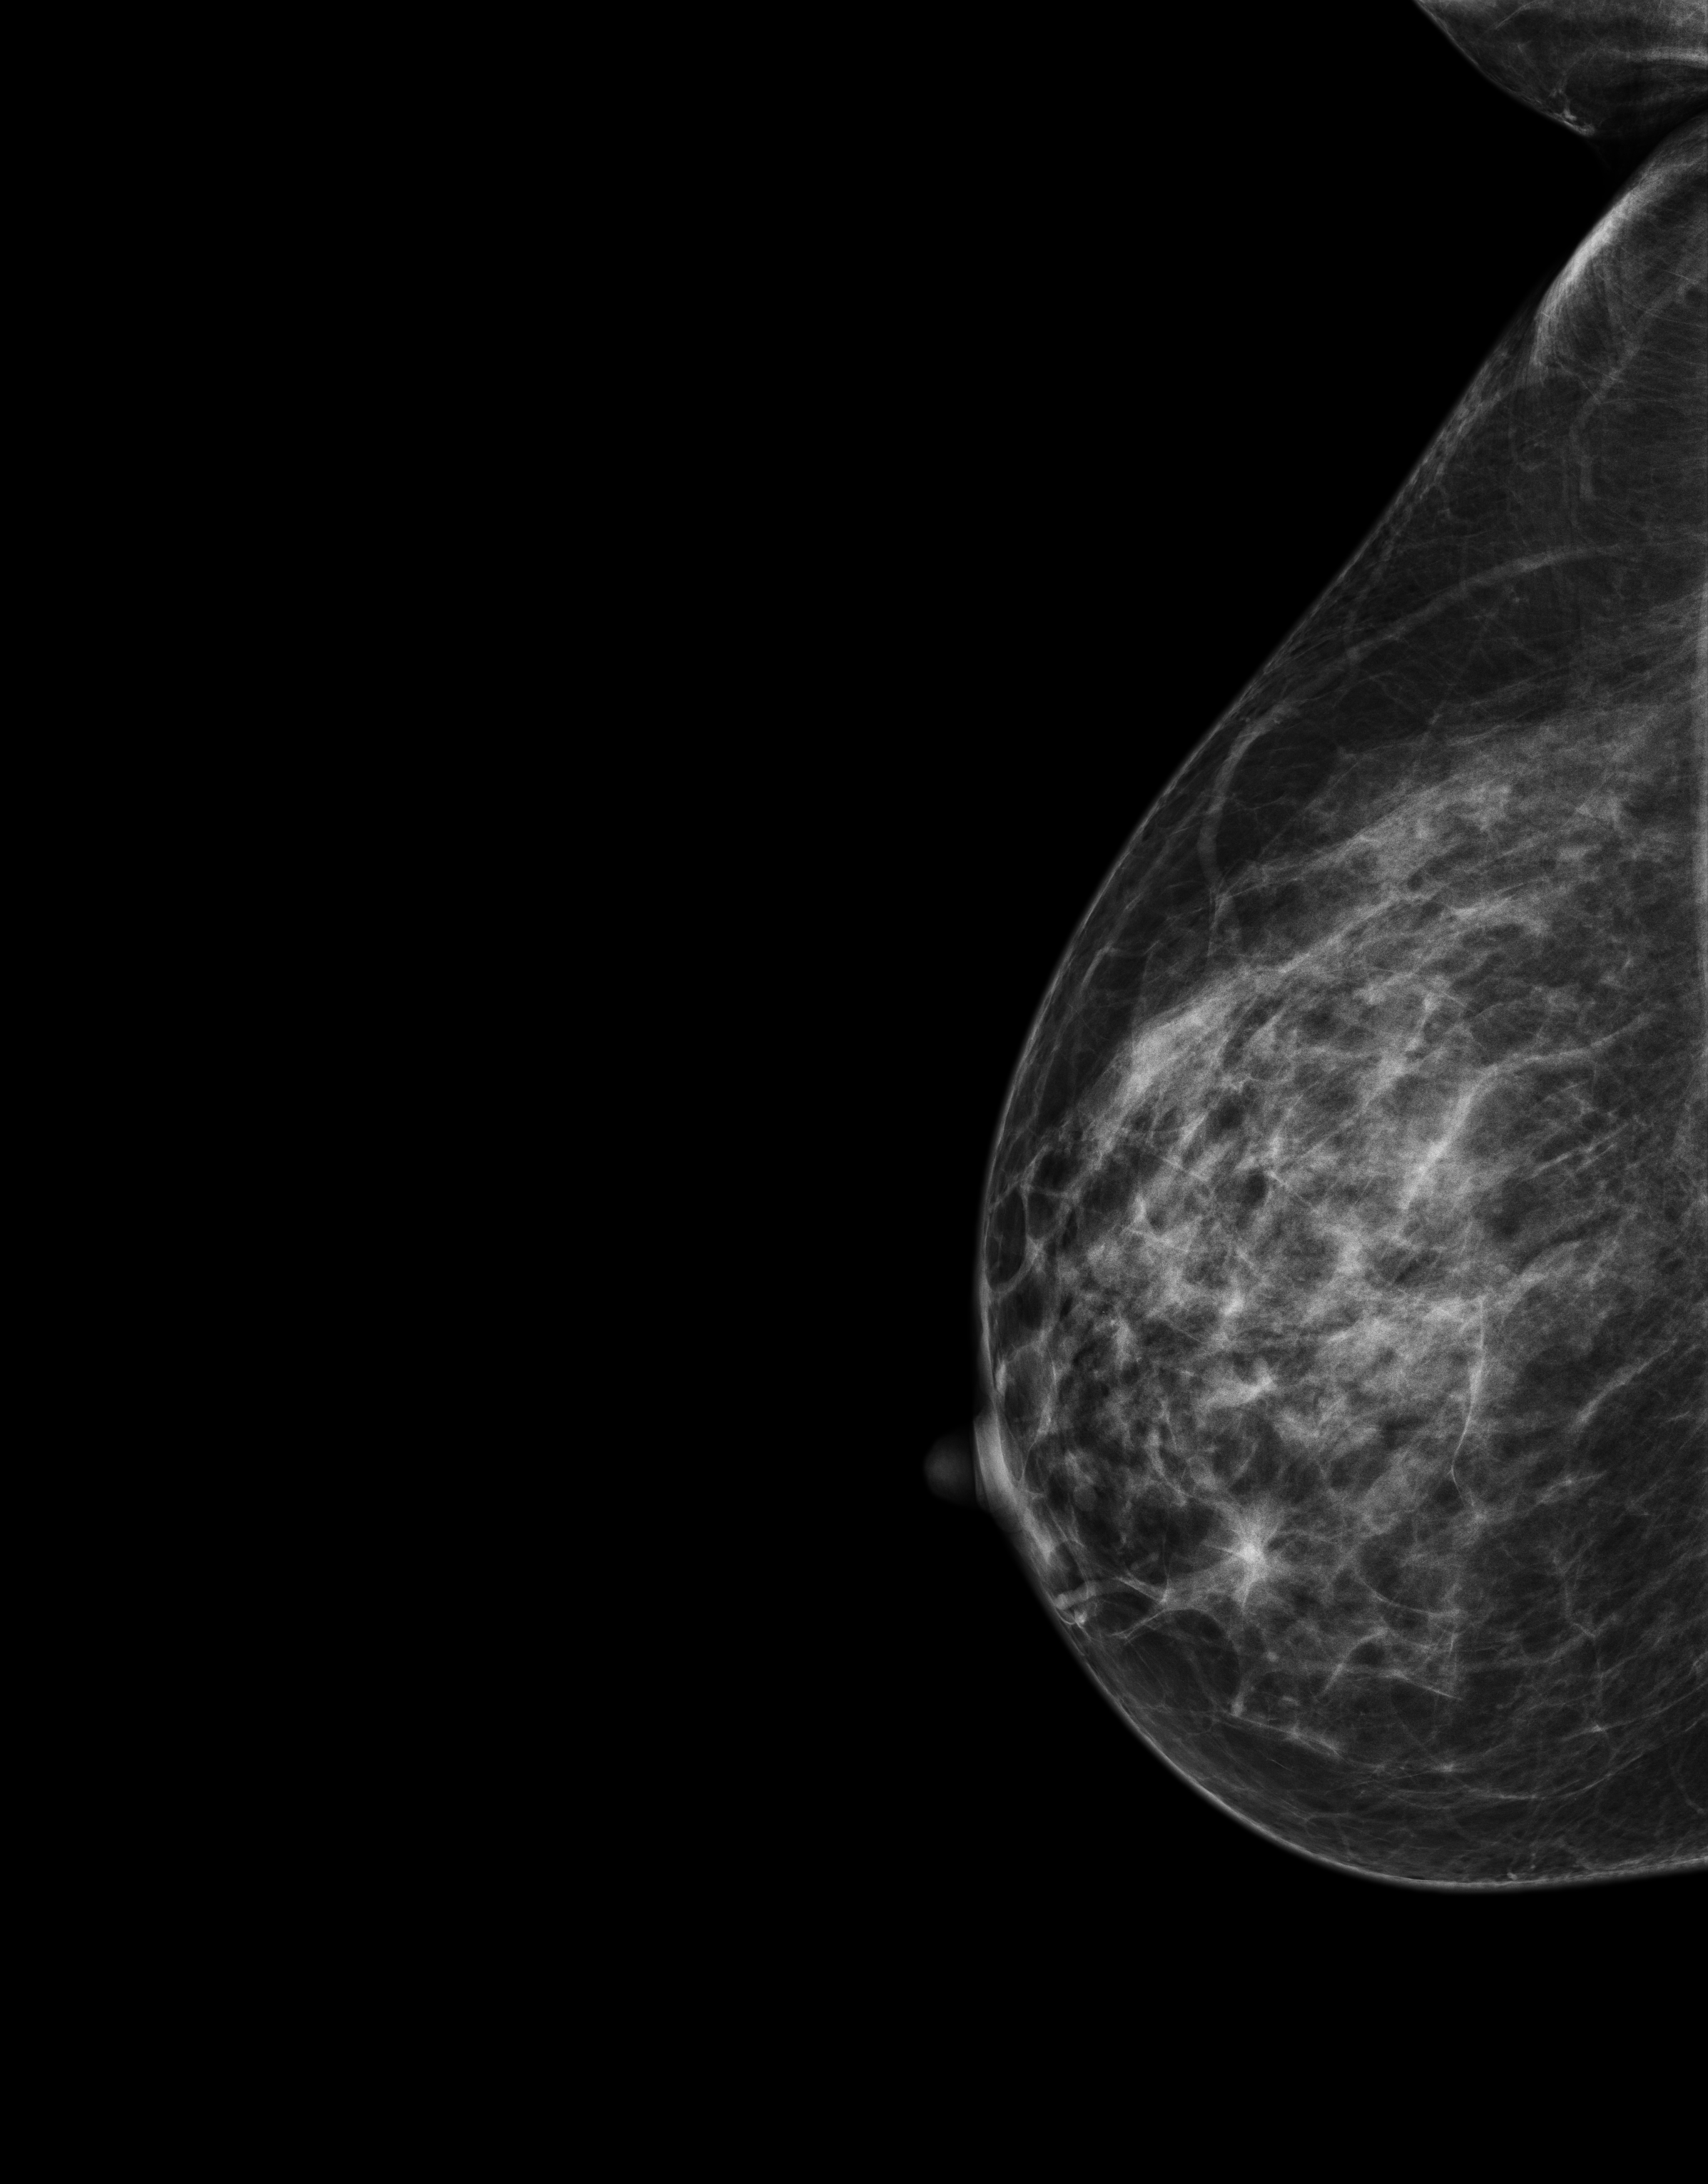
Annual screening mammography examination. Patient: female, 50 years.
Image type: full-field digital mammogram. Breast: right. Projection: laterally exaggerated craniocaudal (XCCL) view.